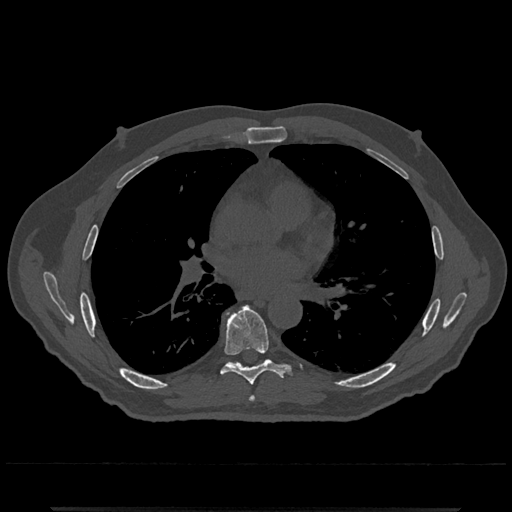
CT including the spine, one axial slice. Slice 719 of 797 in the series (ordered by position). Bone window (W 1800 / L 400 HU). 0.5 mm slice thickness. 512 × 512 image matrix, field of view 393 × 393 mm. Patient: male, 67 years. From the clinical record (not read from this slice): primary cancer: prostate.
Outlined on this slice (semi-automatically segmented with operator editing):
- T6 vertebra: bounding box (x1, y1, x2, y2) in pixels: (249, 396, 255, 402)
- T7 vertebra: (220, 306, 286, 386)